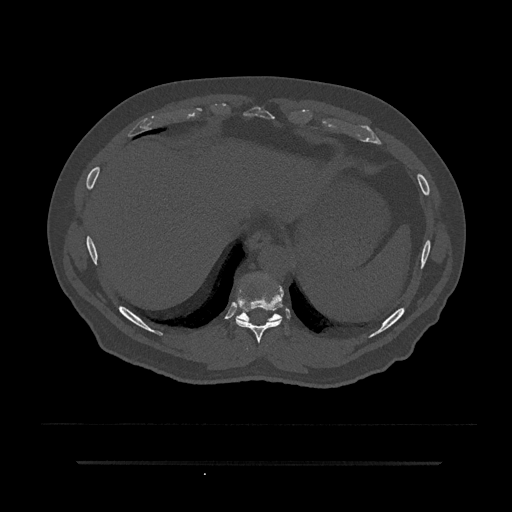
CT including the spine, one axial slice. Position 359 of 797 along the scan axis. Reconstruction kernel Br40s/3. 120 kVp. Bone window (W 1800 / L 400 HU). 512 × 512 image matrix, field of view 464 × 464 mm. Patient: male, 59 years. Case-level facts recorded for this patient, not image findings: primary cancer: bile ducts; vertebrae with lytic lesions (as recorded): T10.
Outlined on this slice (semi-automatic segmentation, software-assisted and operator-edited):
- T10 vertebra: bounding box <235,309,287,335> (left, top, right, bottom; pixels)
- T9 vertebra: <235,279,284,343>